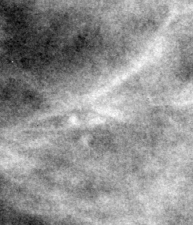
Cropped region of a digitized screen-film mammogram centred on a radiologist-marked abnormality, right breast, CC view.
- Calcifications, morphology amorphous / pleomorphic, distribution clustered; BI-RADS assessment category 4; subtlety rating 2 on a 1 (subtle) to 5 (obvious) scale; pathology result (as recorded, not read from the image): benign.